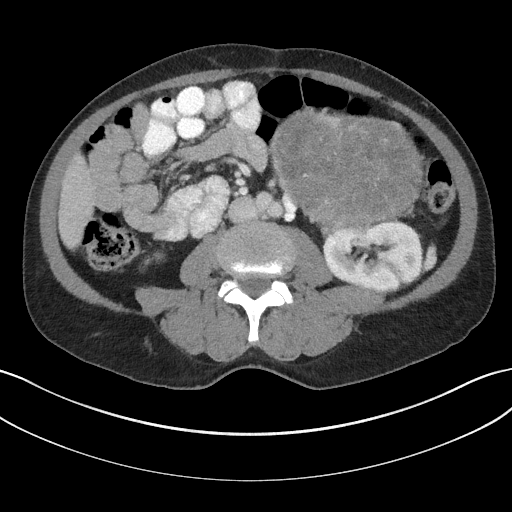
Contrast-enhanced abdominal CT, one axial slice. Slice 79 of 147 in the series (ordered by position). Reconstruction kernel I31f/3. Intravenous contrast given. Soft-tissue window (W 400 / L 40 HU). 512 × 512 image matrix, field of view 384 × 384 mm. Male patient, age 58 years. Case-level facts recorded for this patient, not image findings: diagnosis: adrenocortical carcinoma; tumour side: left adrenal; tumour size at pathology: 22 cm; Ki-67 index: 26 %; stage (as recorded): 2.
Structures marked on this image (semi-automatic segmentation, software-assisted and operator-edited):
- mass: bounding box <274,112,422,226> (left, top, right, bottom; pixels)